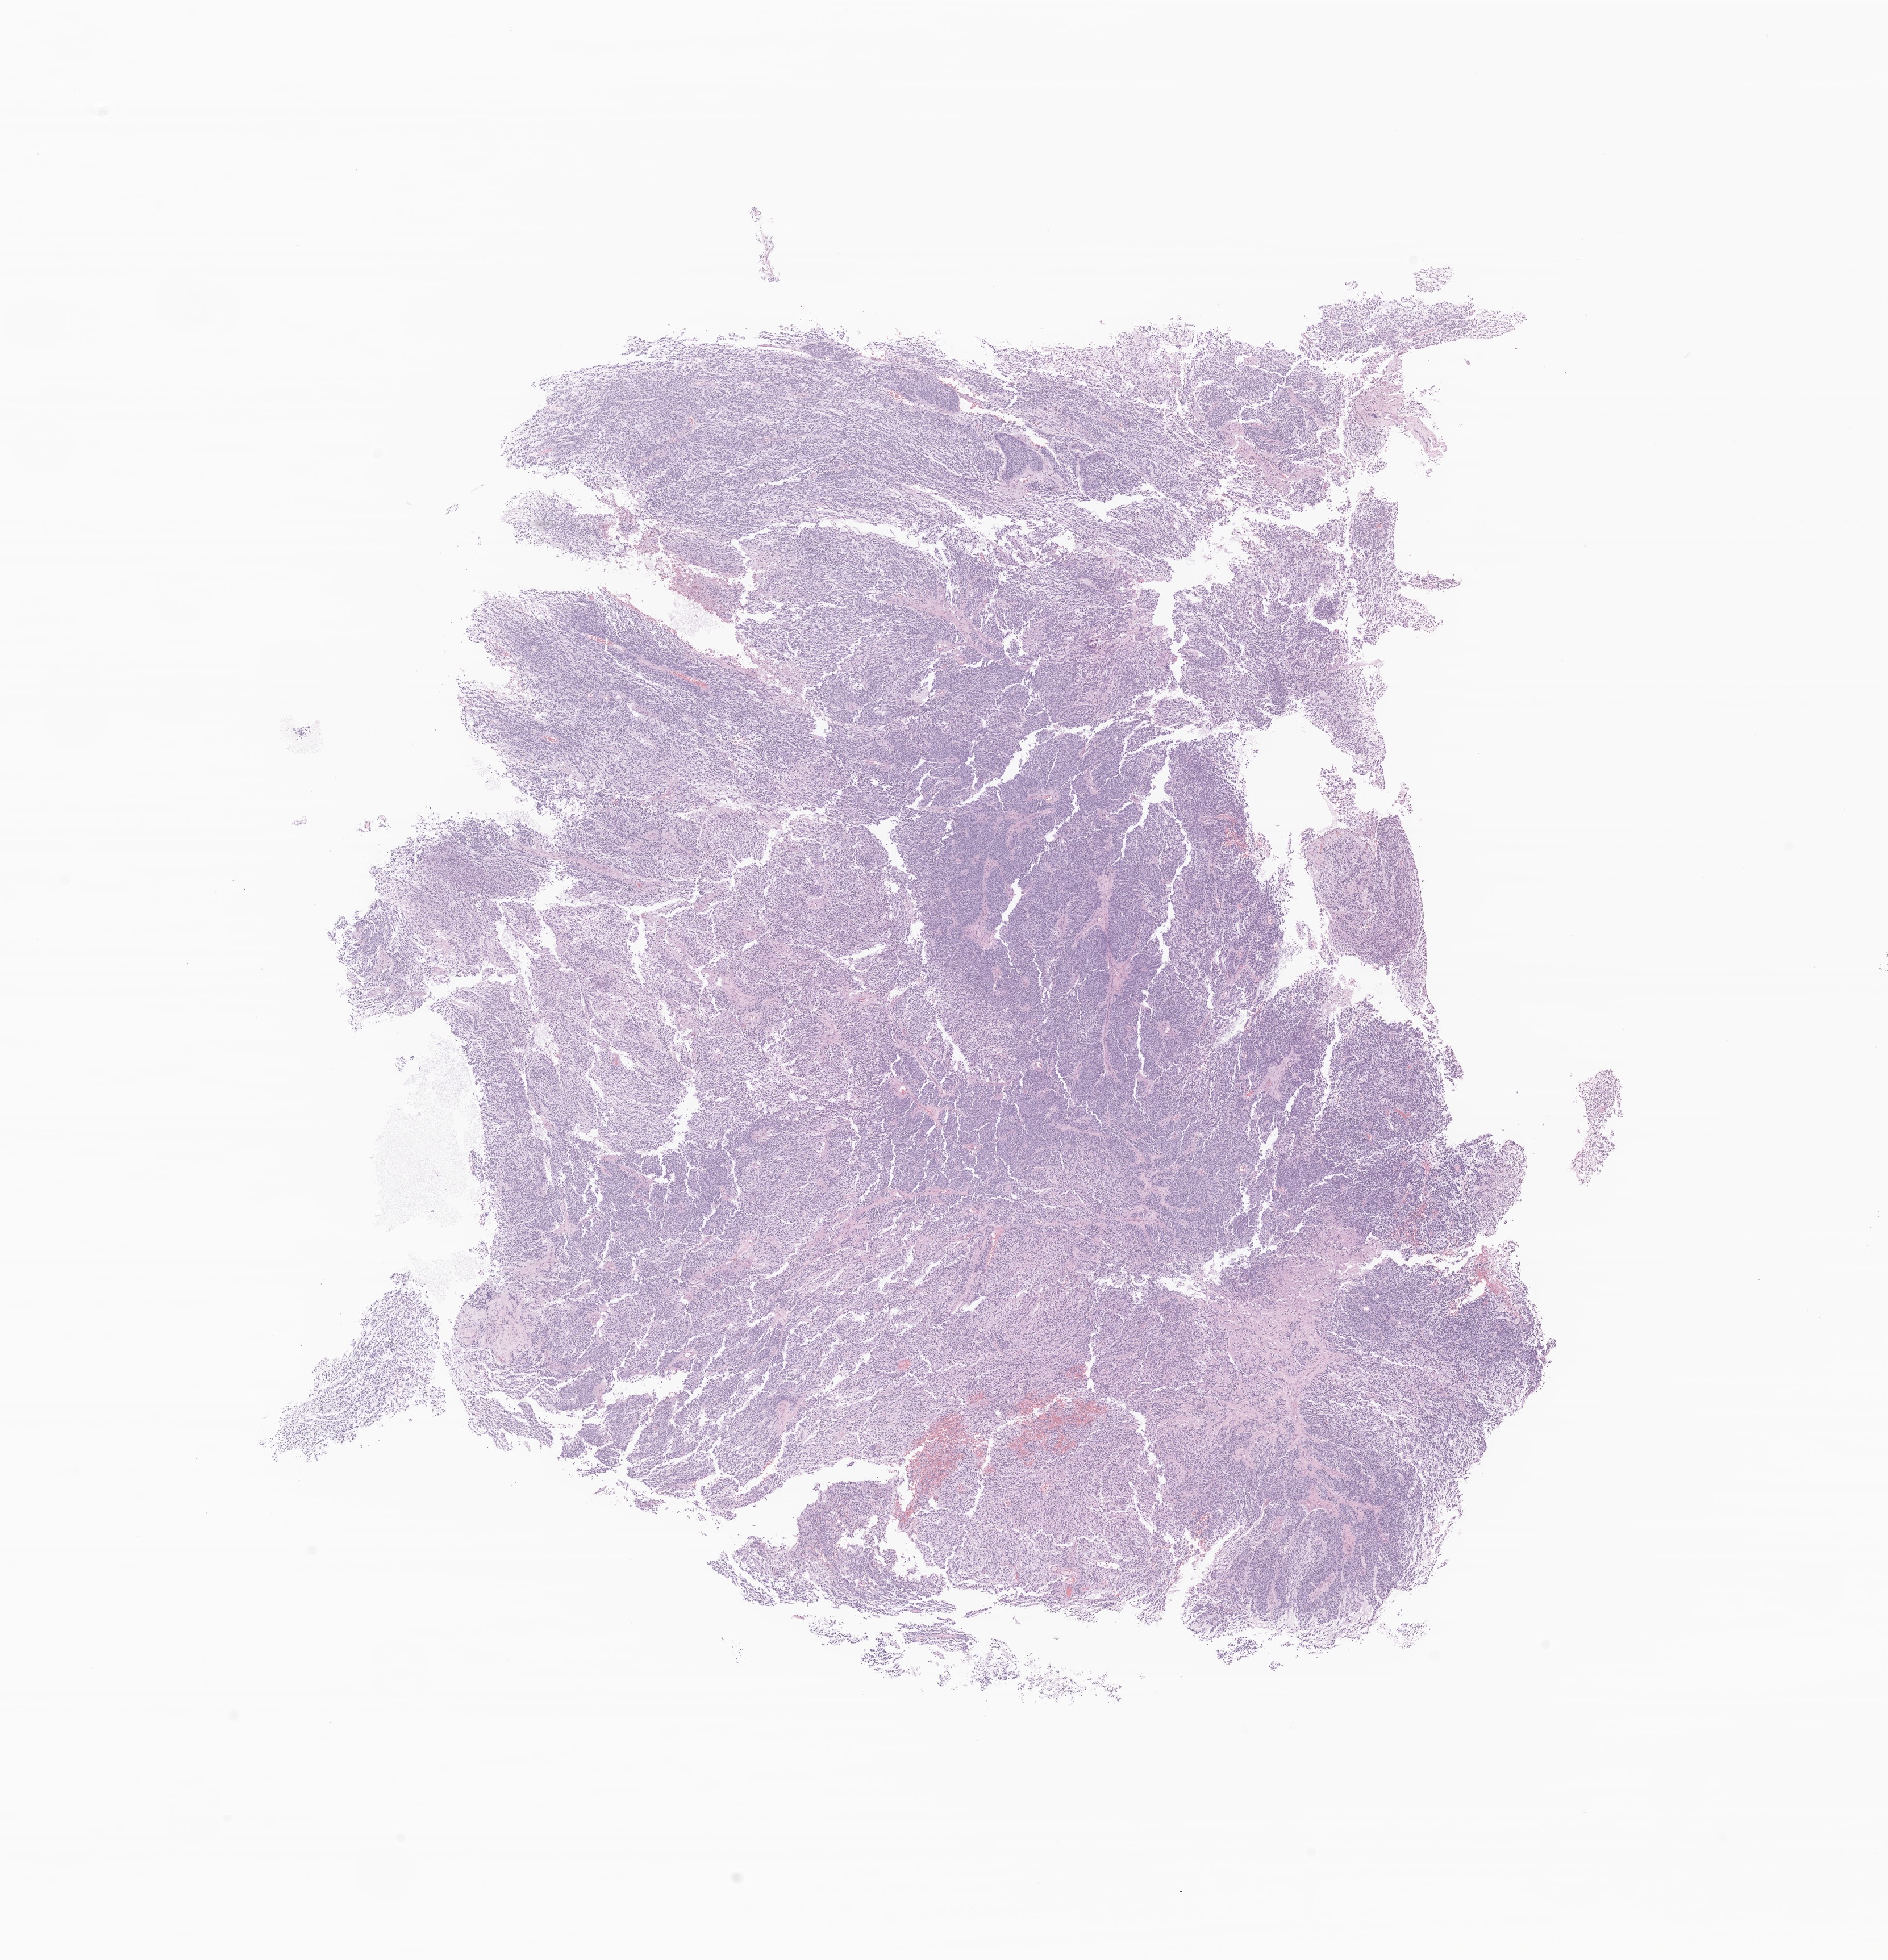
Hematoxylin and eosin (H&E) whole-slide image of tumor tissue from the frontal lobe — whole scanned area (about 14.0 x 14.5 mm) shown as a low-resolution overview; formalin-fixed paraffin-embedded section. Female patient, age 41 months (3 years 5 months).
Recorded diagnosis: Tumor cells, malignant.